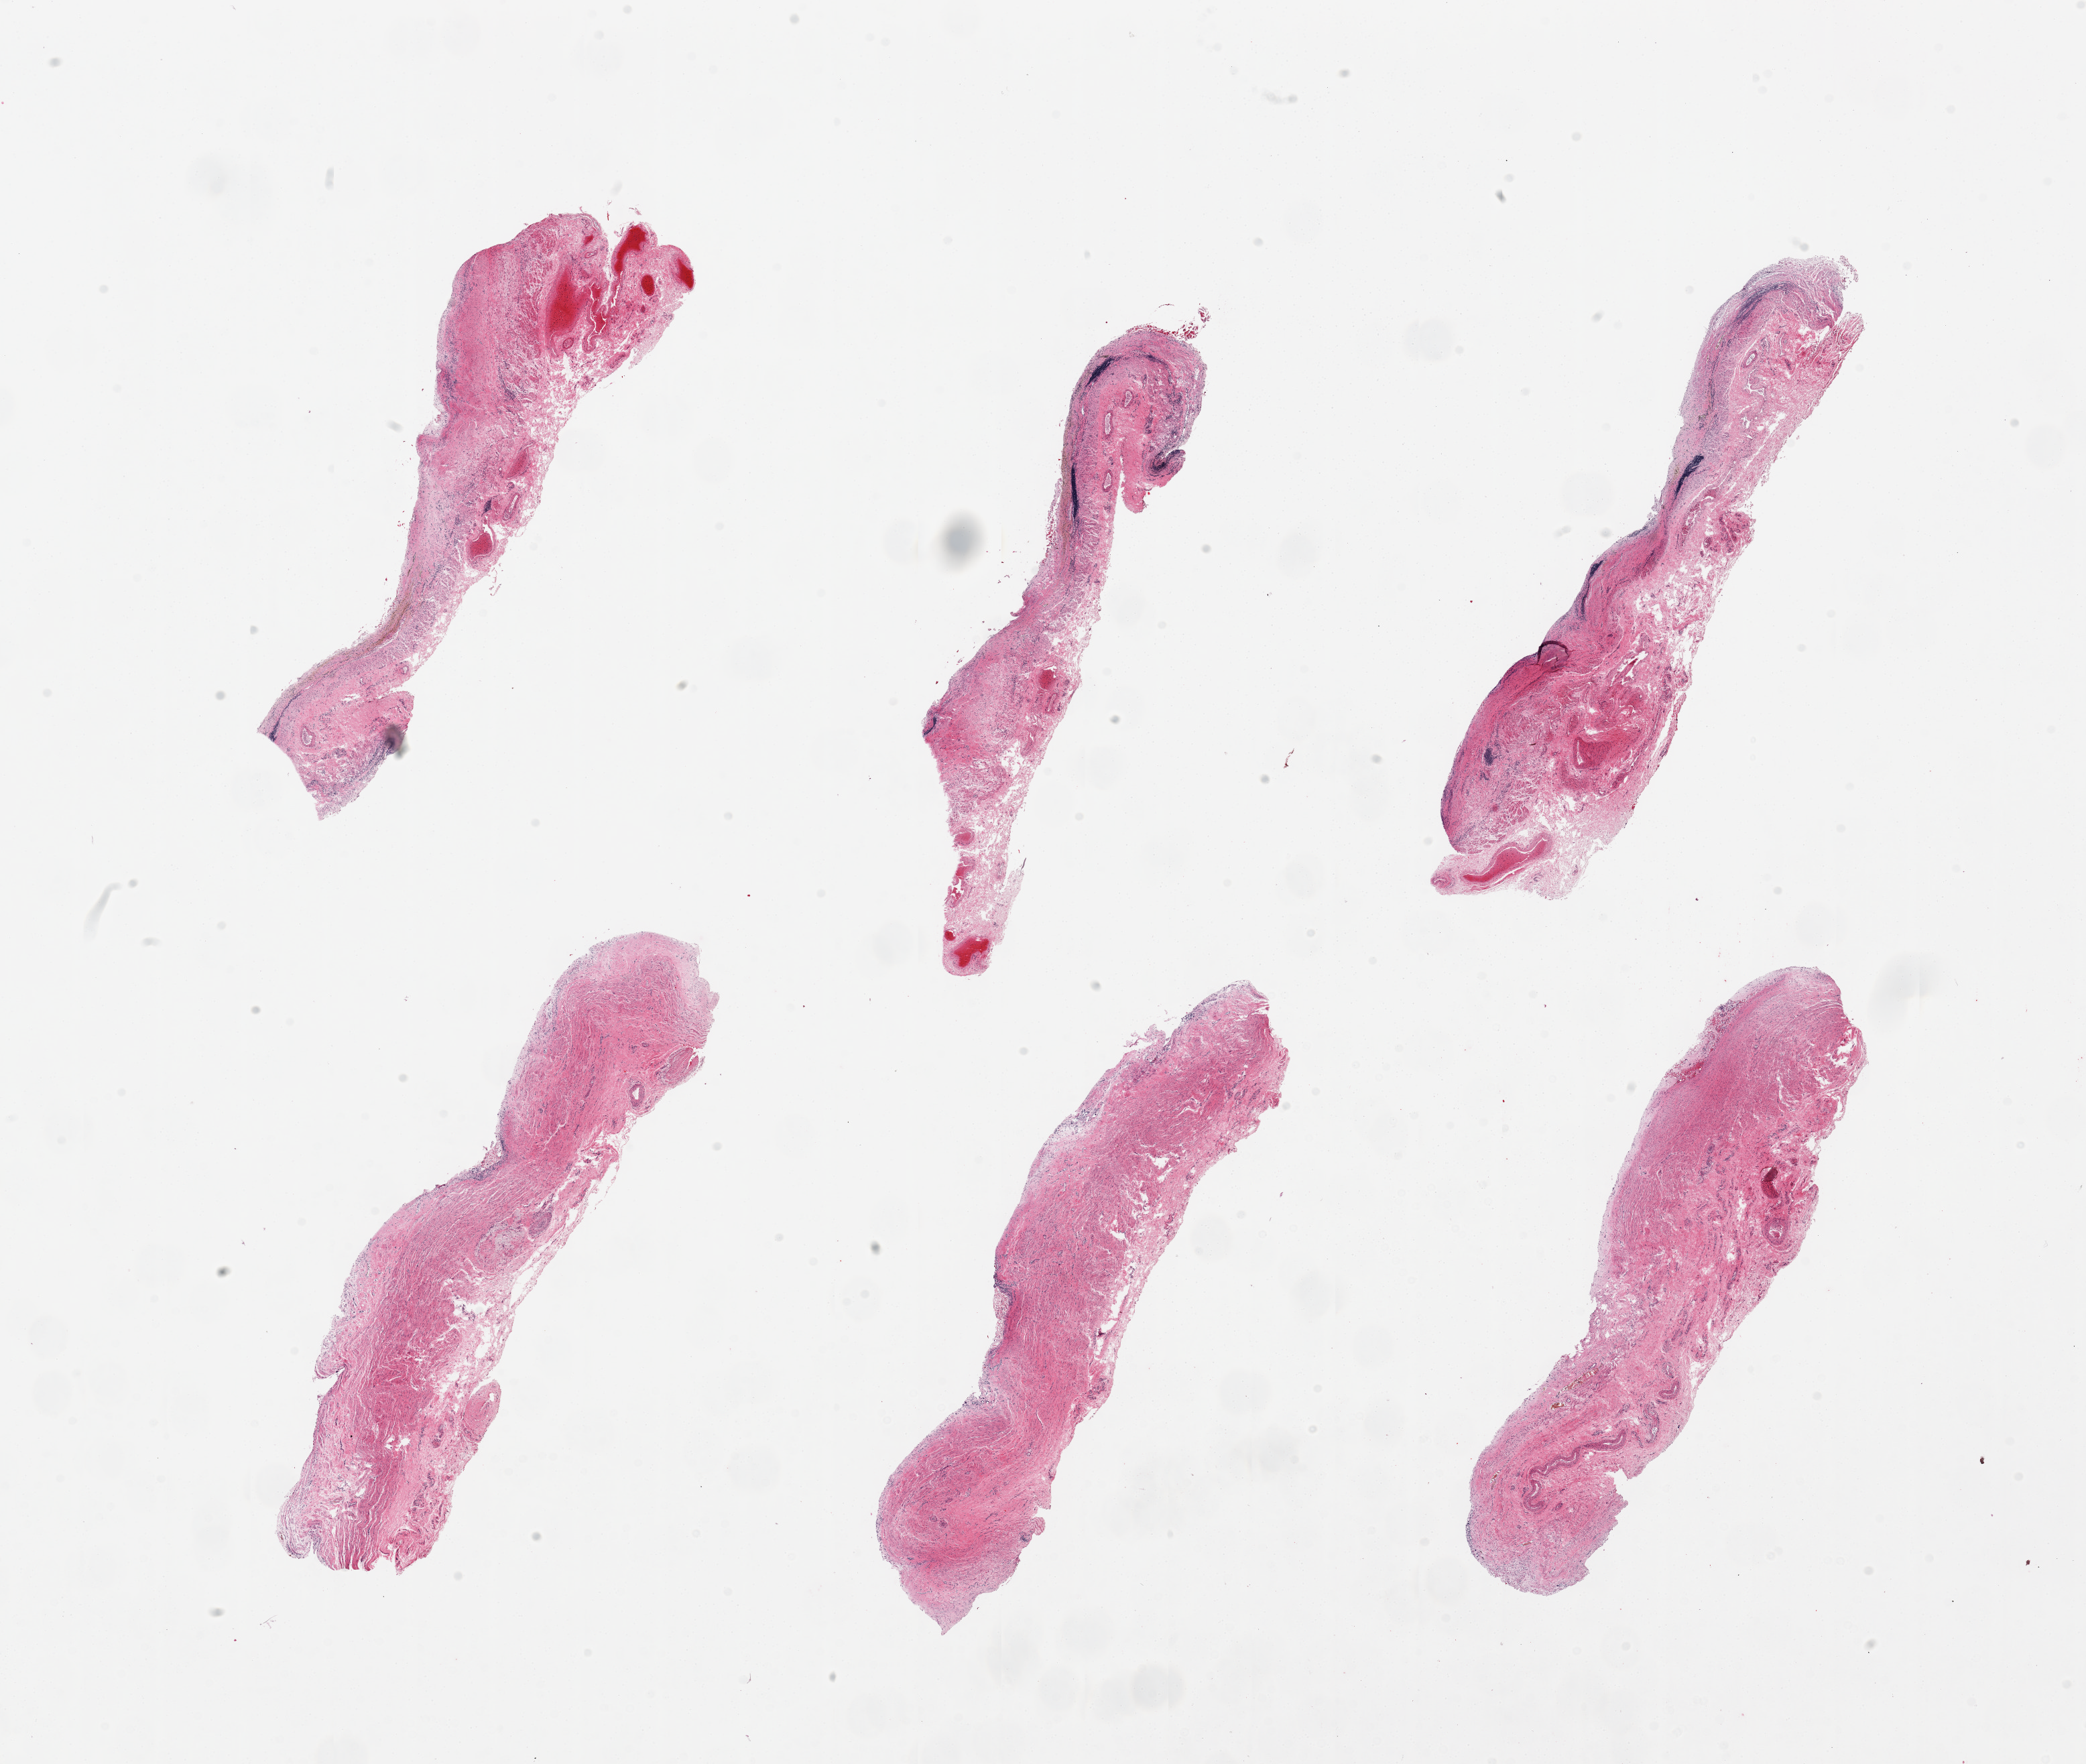
H&E whole-slide image — whole scanned area (about 24.6 x 20.8 mm, slide scanned at 20x) shown as a low-resolution overview, PAXgene-fixed, paraffin-embedded tissue, sampled site (target tissue): gastroesophageal junction, tissue donor sample. Donor: male.
Pathologist's review note for this sample: 6 pieces, mixed fibrofatty/vascular/smooth muscle, not typical of pure esophageal muscularis, so therefore of uncertain provenance.